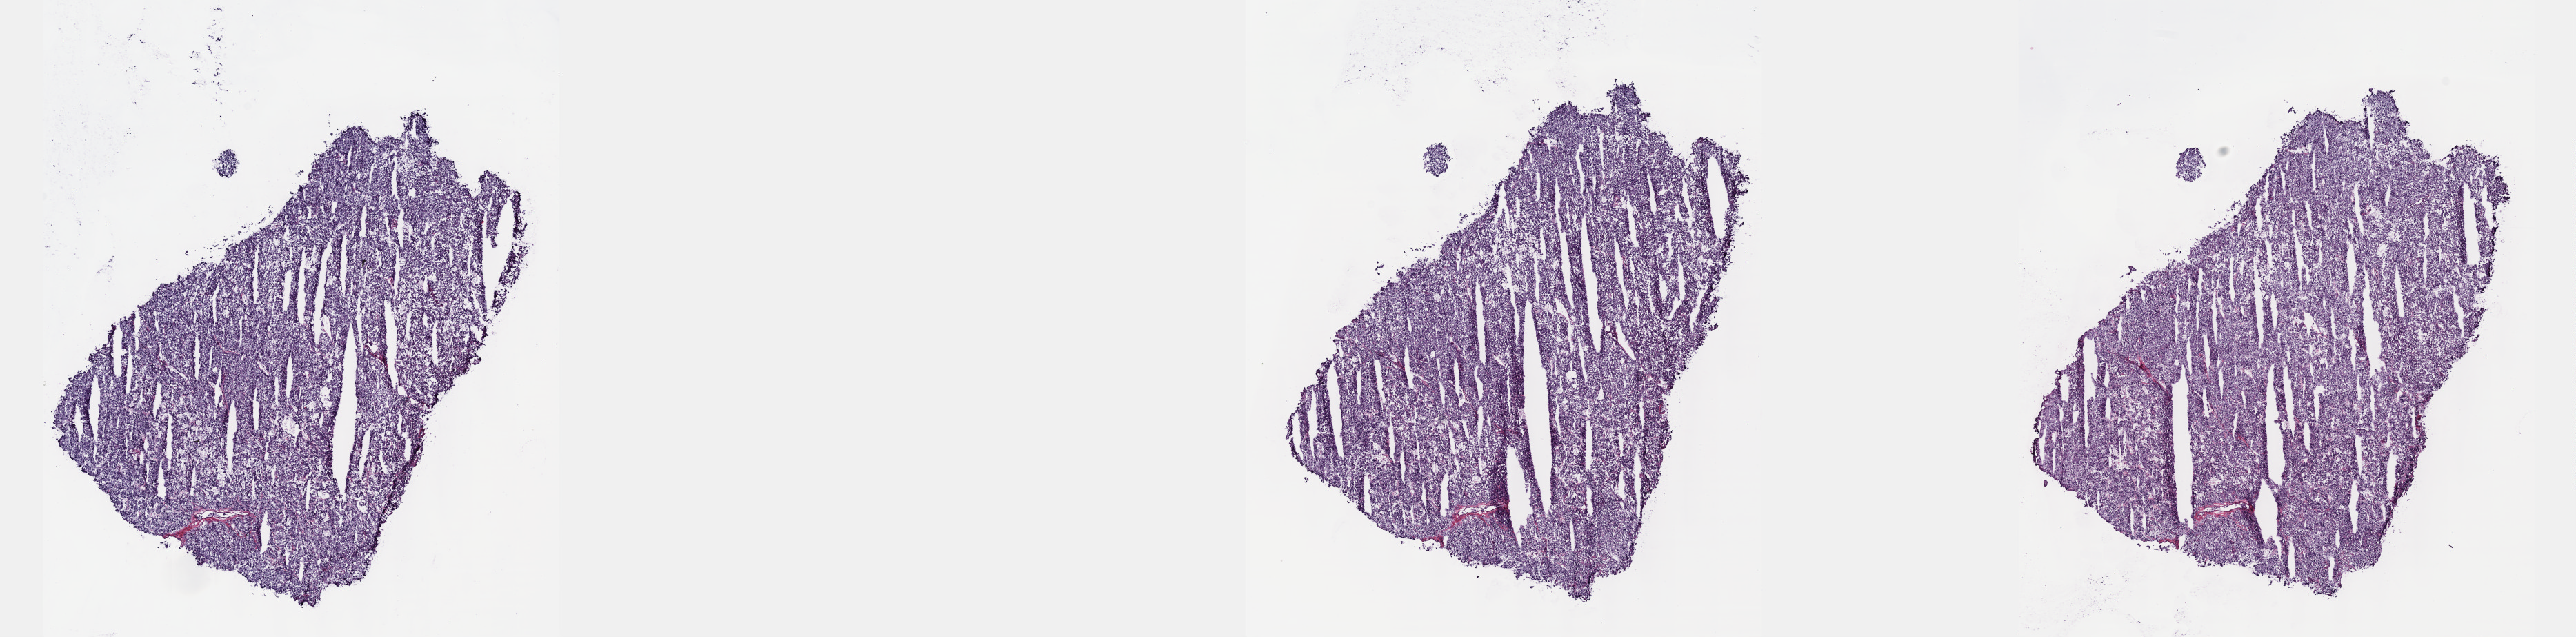
Digitized H&E-stained tissue section (whole slide) — shown as a low-resolution overview of the whole scanned area (about 30.2 x 7.5 mm), frozen section from the top of the tissue portion, primary tumour sample from the adrenal gland. Female, age 25 years at initial diagnosis. Composition of this section per pathologist review: tumour cells 99%, tumour nuclei 99%, normal cells 0%, stromal cells 1%, necrosis 0%. Inflammatory infiltration, as recorded: lymphocyte infiltration 0%, monocyte infiltration 0%, neutrophil infiltration 0%.
• laterality: left
• pathologic diagnosis: Pheochromocytoma, NOS